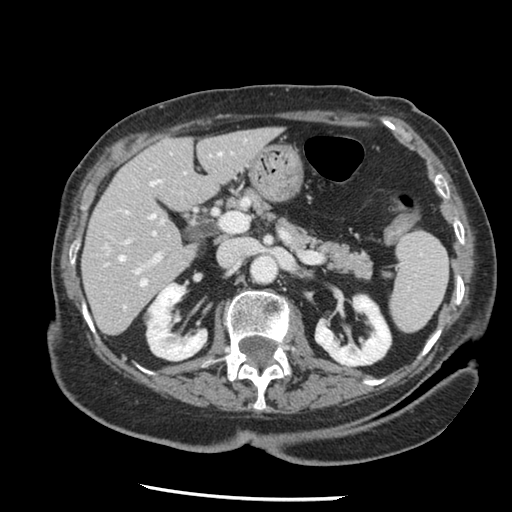
Contrast-enhanced abdominal CT, one axial slice. Position 70 of 148 along the scan axis. 120 kVp. Intravenous contrast given. Soft-tissue window (W 400 / L 40 HU). 512 × 512 image matrix, field of view 330 × 330 mm. Female patient, age 85 years. Case-level facts recorded for this patient, not image findings: diagnosis: colorectal cancer liver metastases, imaged before liver resection; multiple liver metastases: no; largest metastasis: 0.9 cm; disease in both lobes: no.
Annotated regions visible in this slice (expert manual segmentation):
- hepatic veins: bounding box [x1, y1, x2, y2] px = [119, 152, 173, 286]
- liver: [83, 129, 279, 334]
- planned liver remnant (the part of the liver to remain after resection): [83, 129, 279, 333]
- portal vein (with intrahepatic branches): [125, 150, 224, 276]